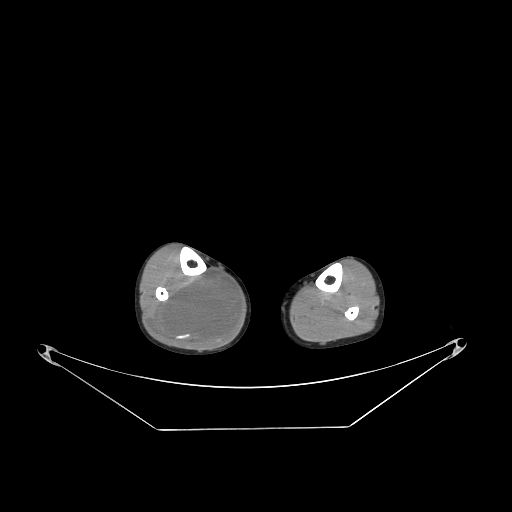
CT of an extremity soft-tissue mass (from a PET/CT study), one axial slice; position 97 of 267 along the scan axis; 140 kVp; soft-tissue window (W 400 / L 40 HU); 3.75 mm slice thickness; 512 × 512 image matrix, field of view 500 × 500 mm. Male patient. Case-level facts recorded for this patient, not image findings: histological type: liposarcoma - round cell; grade: high; site of the primary tumour: right calf.
Structures marked on this image (expert contour drawn on MRI and transferred to this co-registered scan by the dataset authors):
- gross tumour volume (mass): box from (x=151, y=270) to (x=241, y=350) px